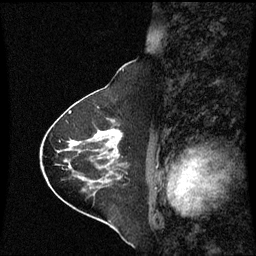
Breast MRI (dynamic contrast-enhanced), one sagittal slice. Position 29 of 60 along the scan axis. Dynamic contrast-enhanced series, image 2 of 3 at this slice position (ordered by acquisition). 1.5 T. TE 4.2 ms, TR 8.9 ms. 2 mm slice thickness. 256 × 256 image matrix, field of view 210 × 210 mm. Female patient, age 63 years. From the clinical record (not read from this slice): setting: breast cancer imaged before/during neoadjuvant chemotherapy; receptor status: HR-positive, HER2-negative.
Annotated regions visible in this slice (semi-automatically segmented with operator editing):
- analysis volume of interest (the breast-tissue region the enhancement analysis was run in; not a lesion): bounding box (x1, y1, x2, y2) in pixels: (88, 120, 124, 163)
- tumour enhancement mask (voxels above the 70 % enhancement threshold inside the analysis volume of interest): (111, 130, 120, 140)